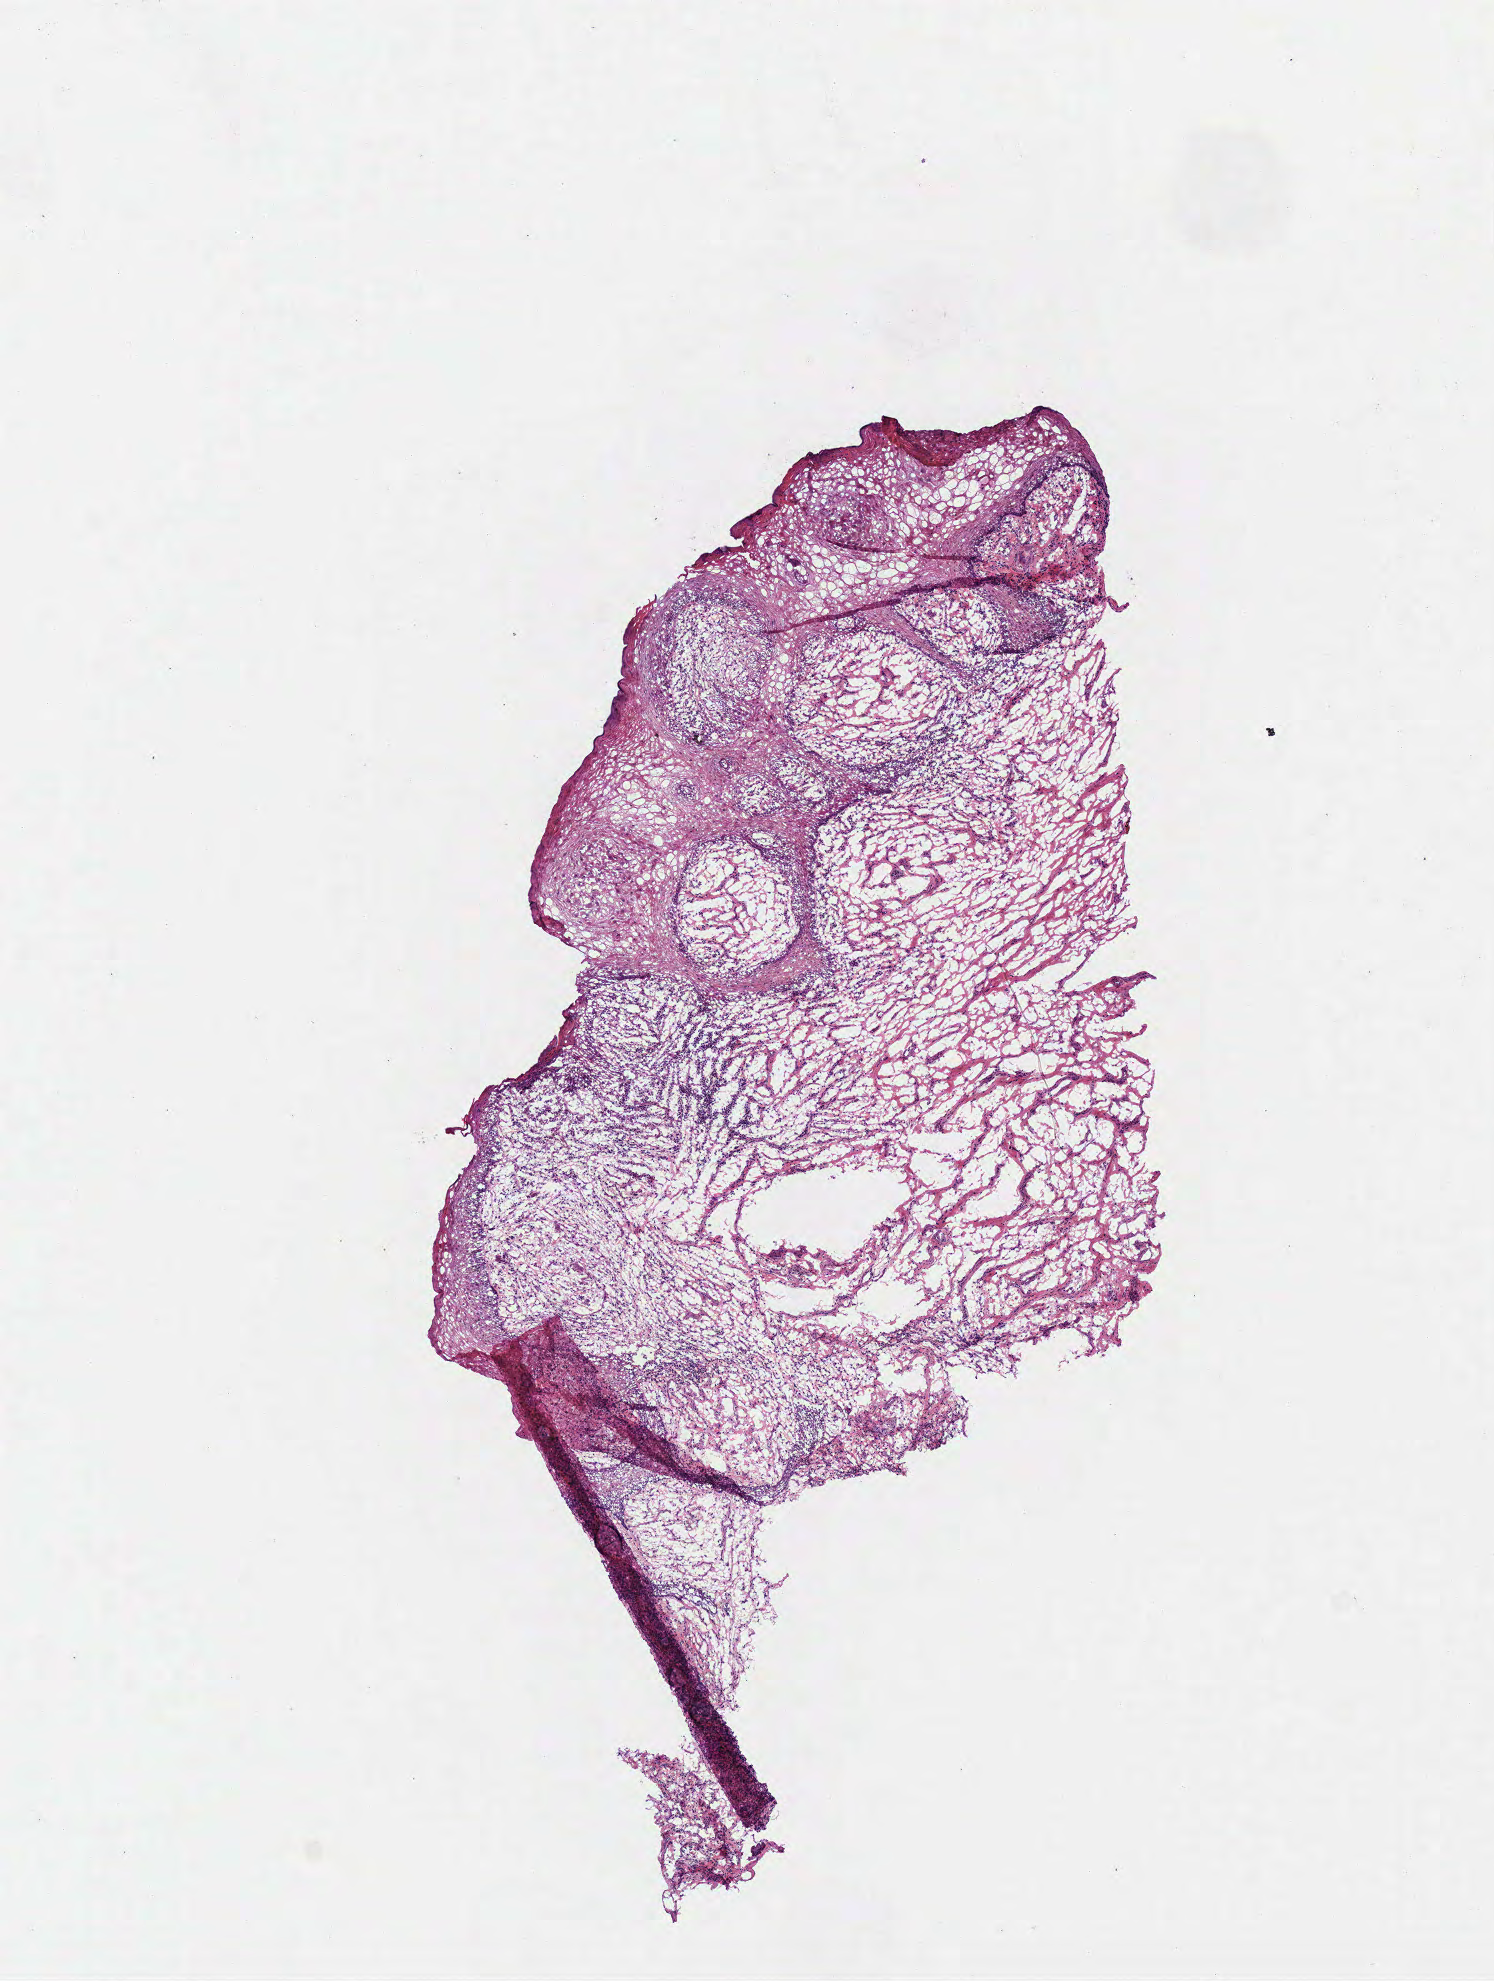
H&E whole-slide image — whole scanned area (about 5.9 x 7.8 mm, acquisition: 40x scan) shown as a low-resolution overview. Frozen section from the top of the tissue portion. Sample: solid tissue normal (non-tumour tissue), head and neck. Male patient; age at initial diagnosis 49 years.
This section: solid tissue normal sample (biorepository sample class). Patient diagnosis: Squamous cell carcinoma, NOS (tongue, NOS).